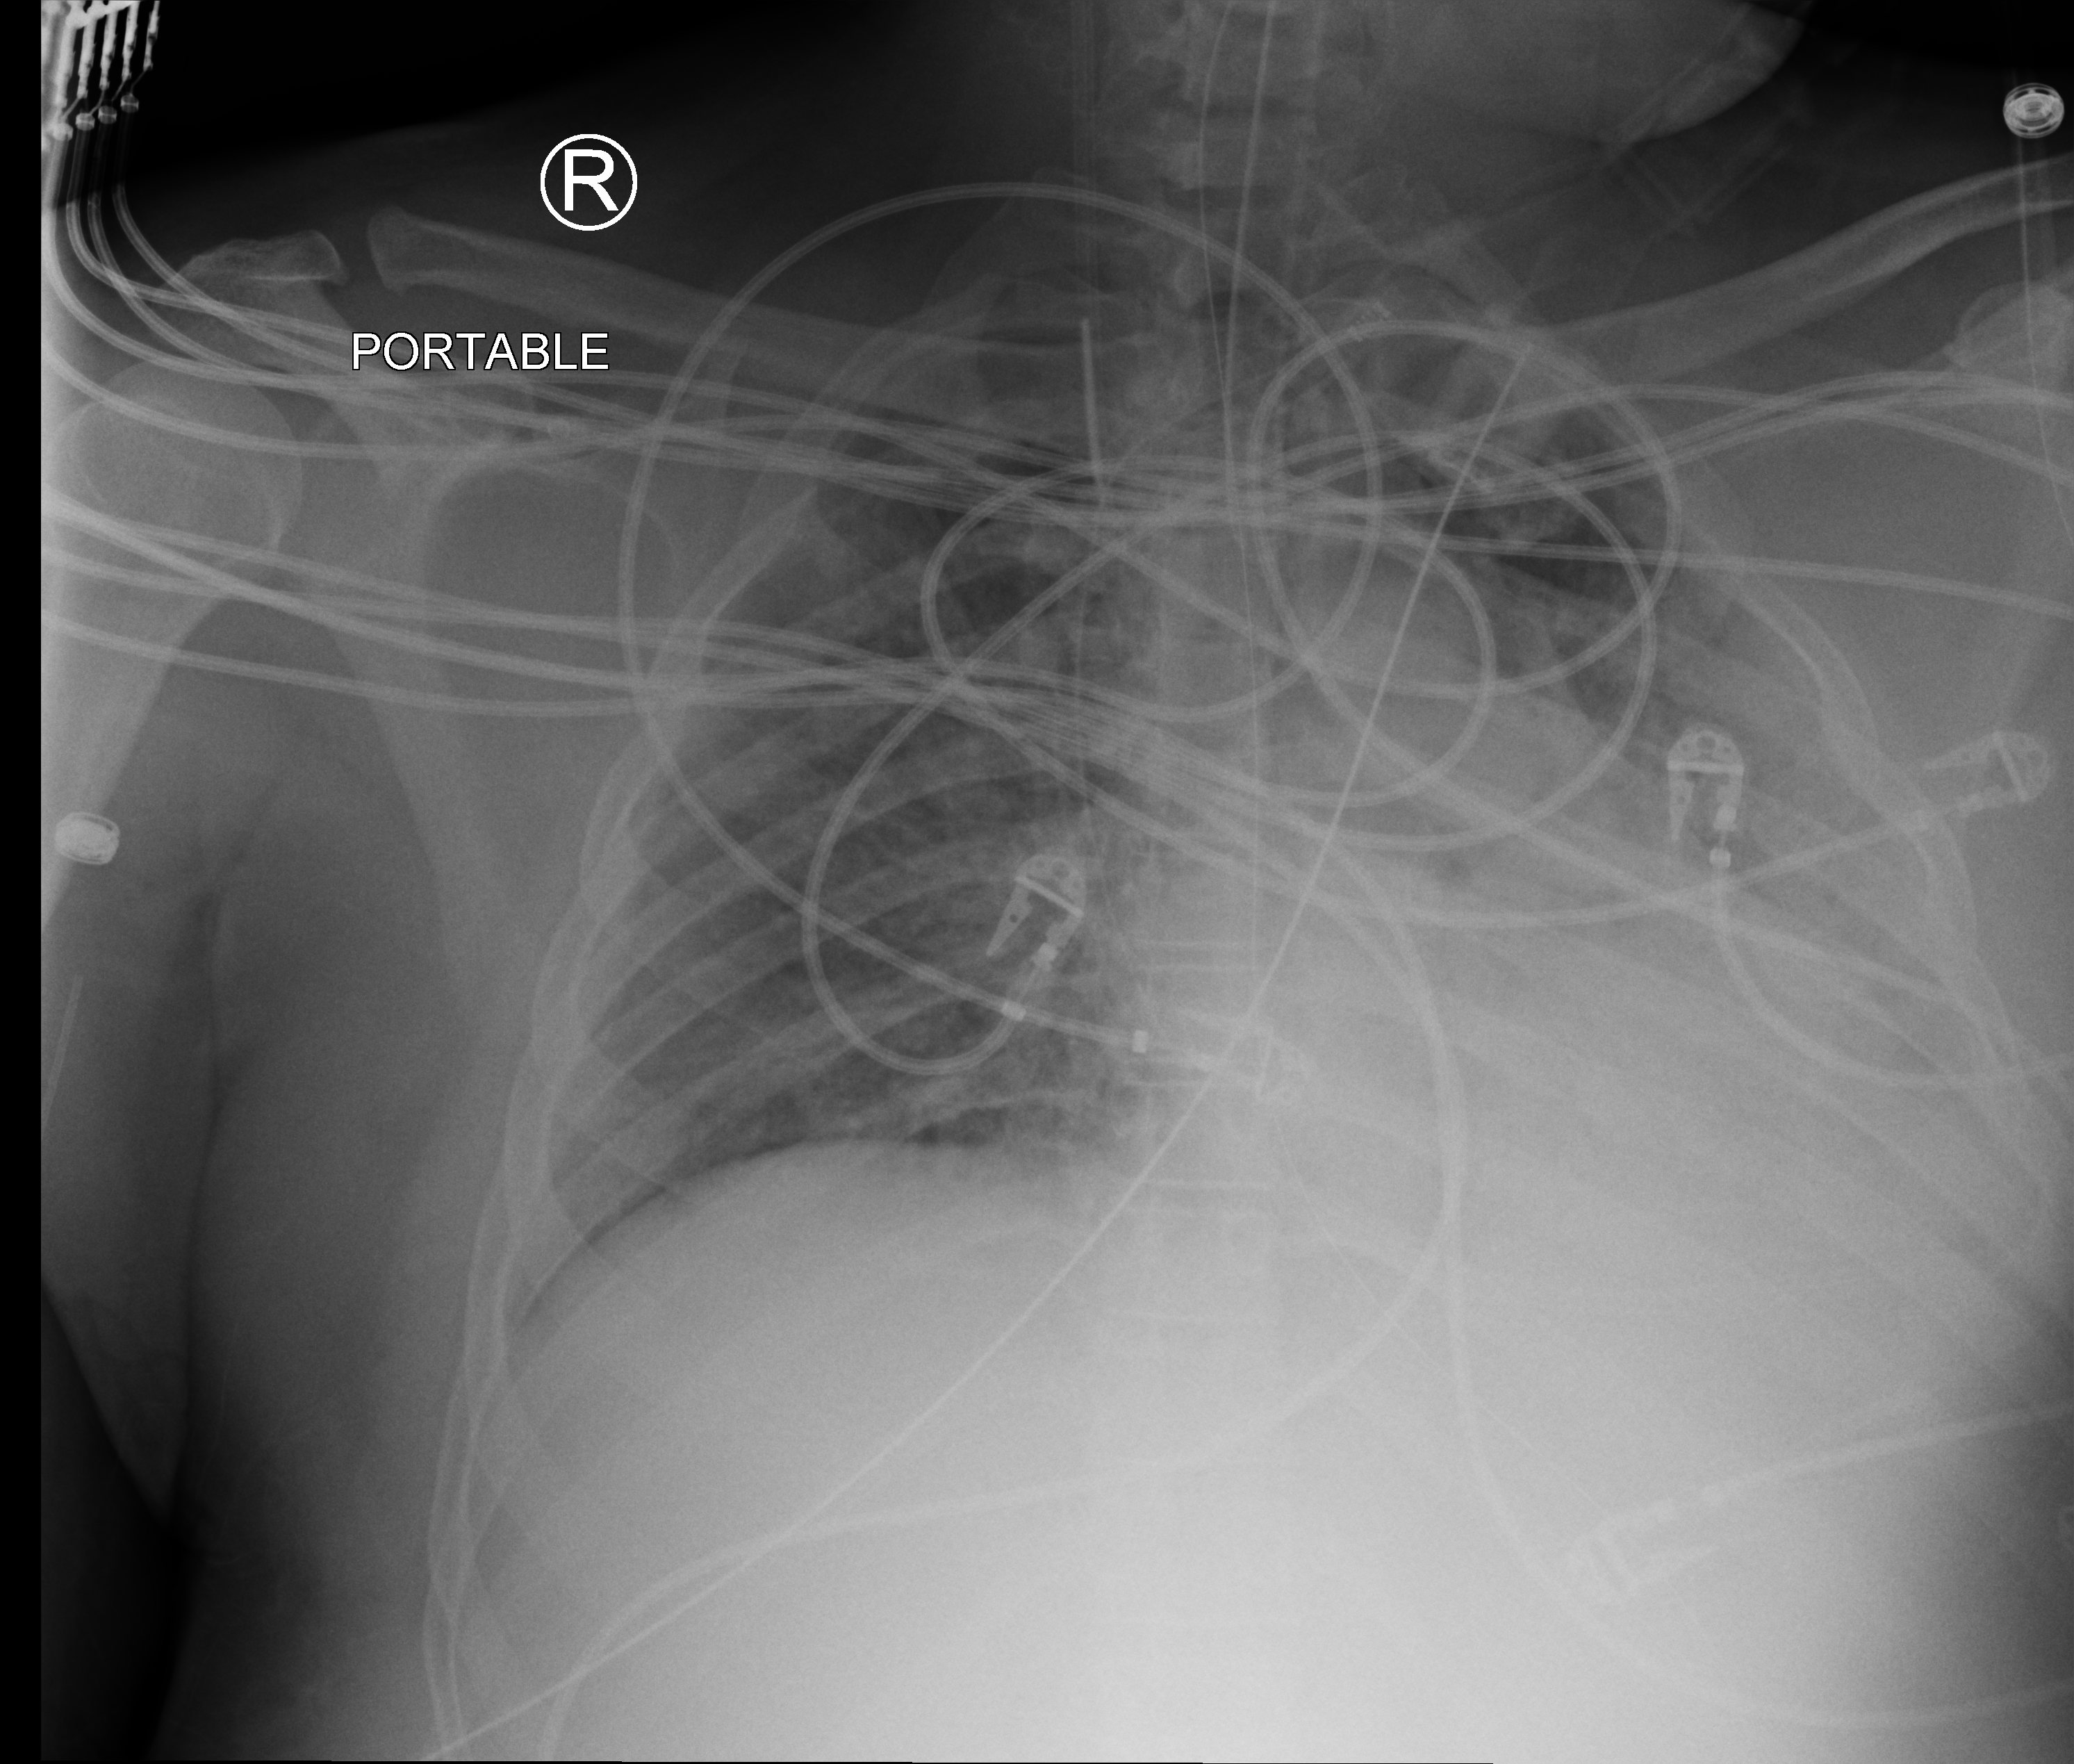
Bedside chest radiograph (computed radiography), anteroposterior (AP) projection. Adult patient hospitalised with COVID-19, age 18–59 years.
Admission-level facts for this patient (not findings on this image; timing relative to this image not recorded):
- smoking status (admission record): never